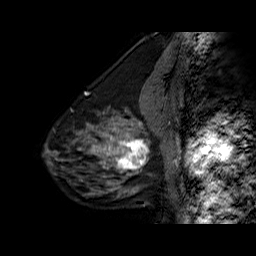
Breast MRI (dynamic contrast-enhanced), one sagittal slice. Slice 22 of 60 in the series (ordered by position). Dynamic contrast-enhanced series, time point 2 of 6 at this slice position (early post-contrast). 1.5 T. TE 6.3 ms, TR 32.5 ms. 256 × 256 image matrix, field of view 200 × 200 mm. Female patient. Case-level facts recorded for this patient, not image findings: setting: breast cancer imaged before/during neoadjuvant chemotherapy; receptor status: triple-negative.
Outlined on this slice (semi-automatic segmentation, software-assisted and operator-edited):
- analysis volume of interest (the breast-tissue region the enhancement analysis was run in; not a lesion): bounding box (x1, y1, x2, y2) in pixels: (108, 126, 154, 177)
- tumour enhancement mask (voxels above the 100 % enhancement threshold inside the analysis volume of interest): (108, 127, 149, 170)